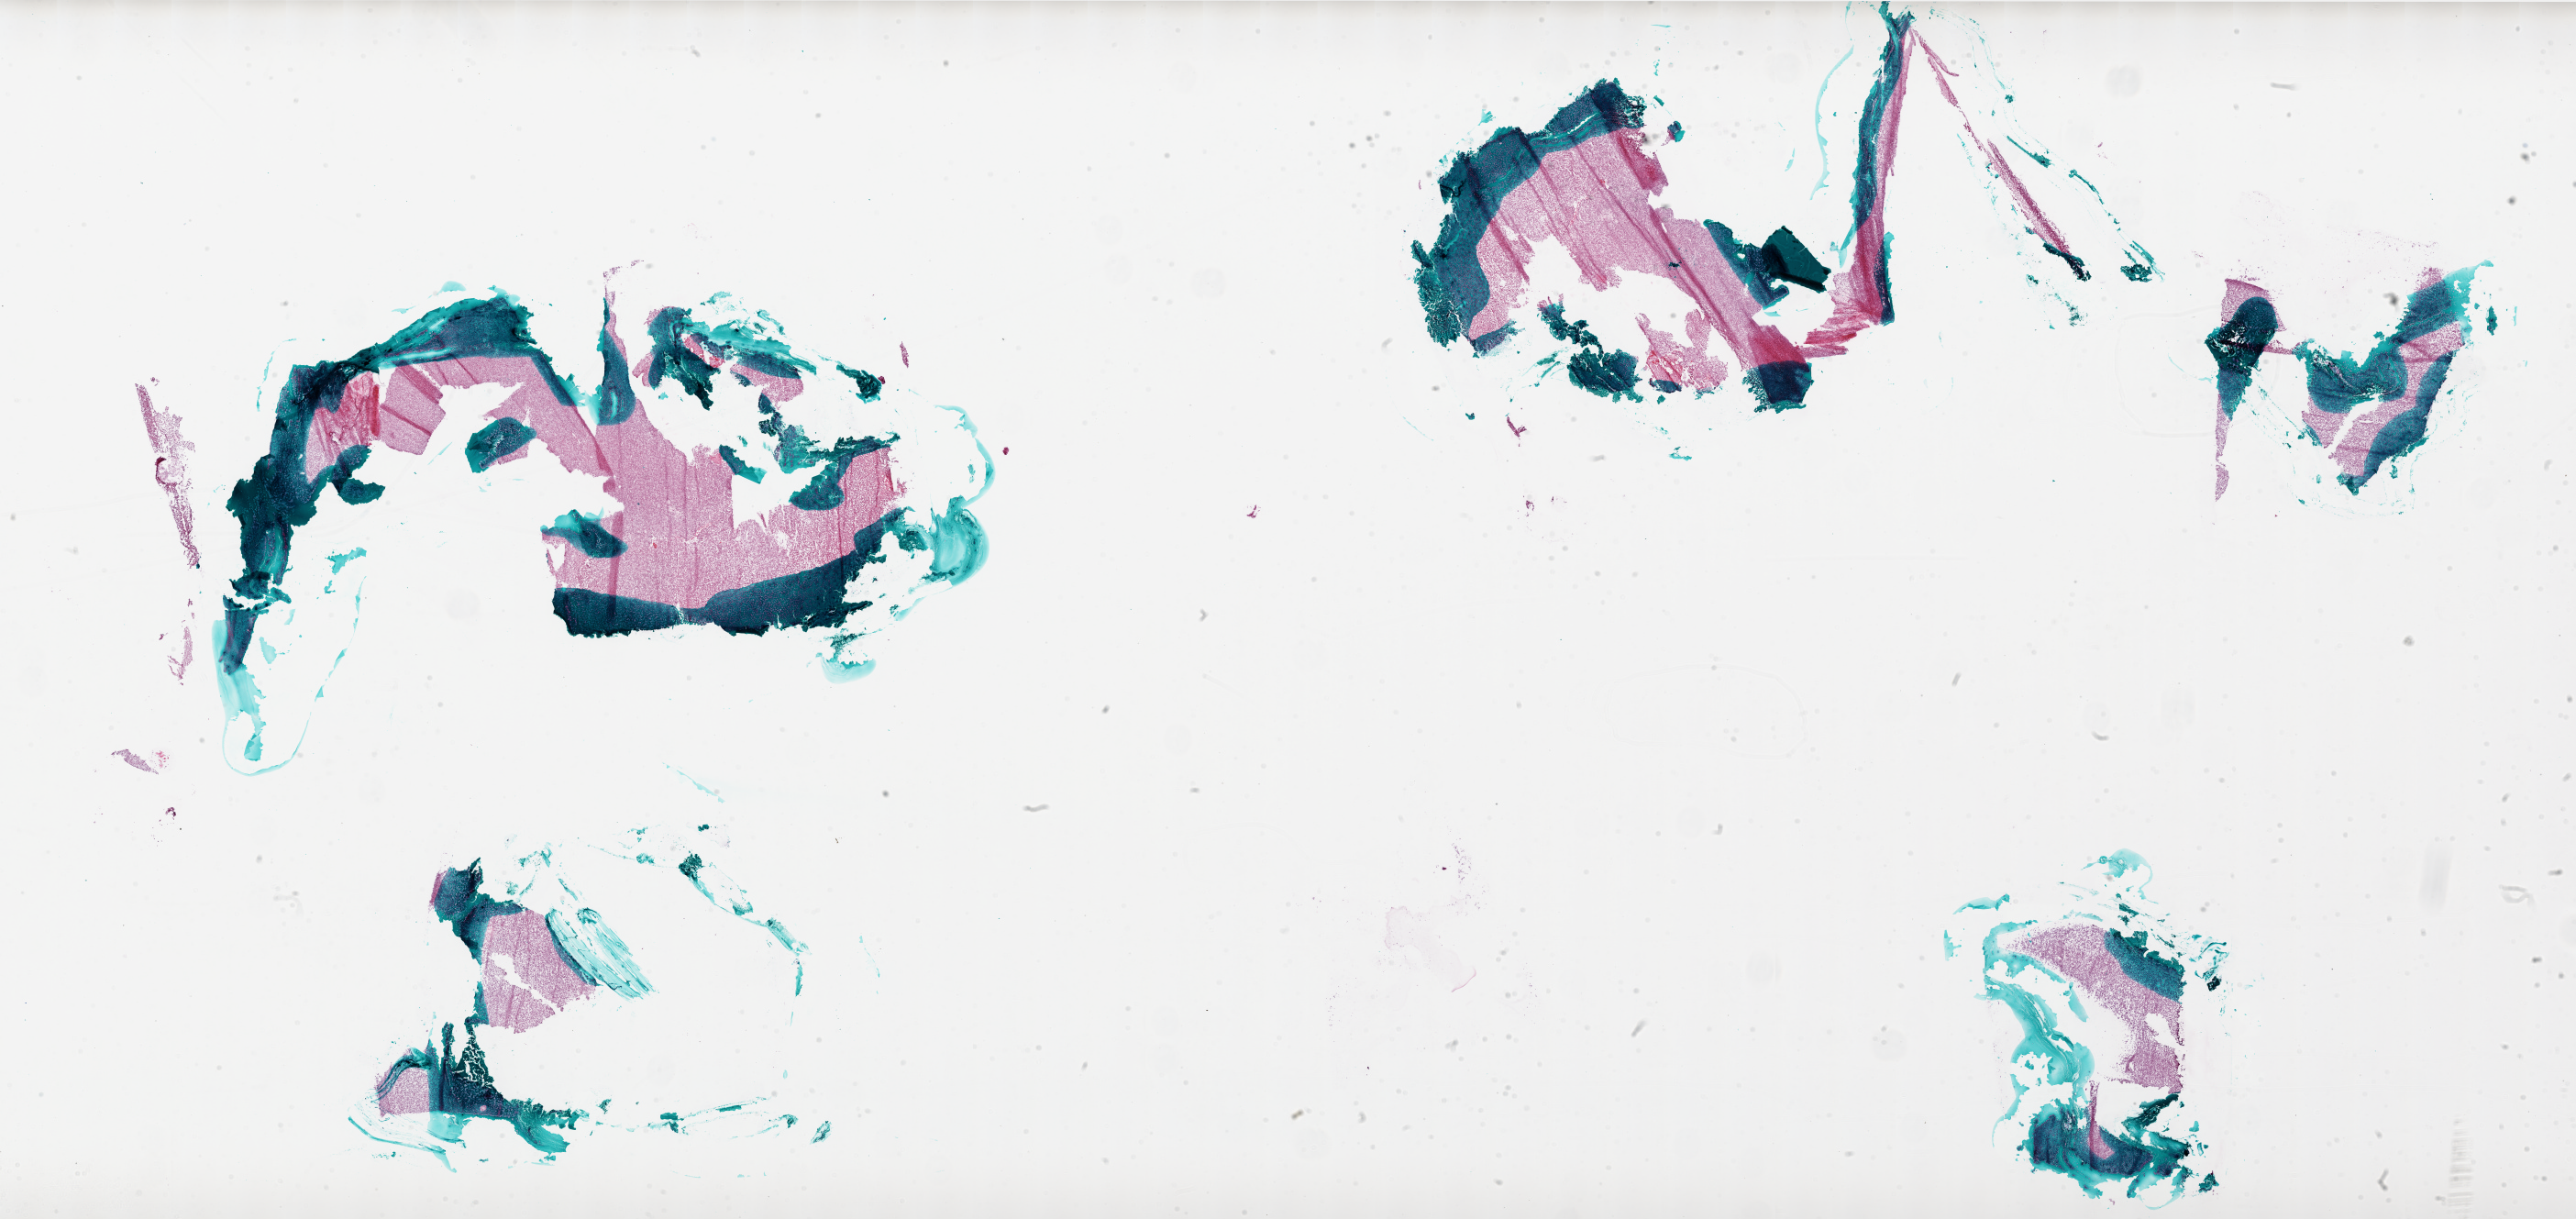
Whole-slide histology image, Hematoxylin and eosin (H&E) stained, whole scanned area (about 45.0 x 21.3 mm, slide scanned at 20x) shown as a low-resolution overview; frozen section from the bottom of the tissue portion; sample: primary tumour, brain. Female patient; age at initial diagnosis 43 years. Composition of this section per pathologist review: tumour cells 95%, tumour nuclei 100%, normal cells 0%, stromal cells 0%, necrosis 5%.
• pathologic diagnosis: Glioblastoma